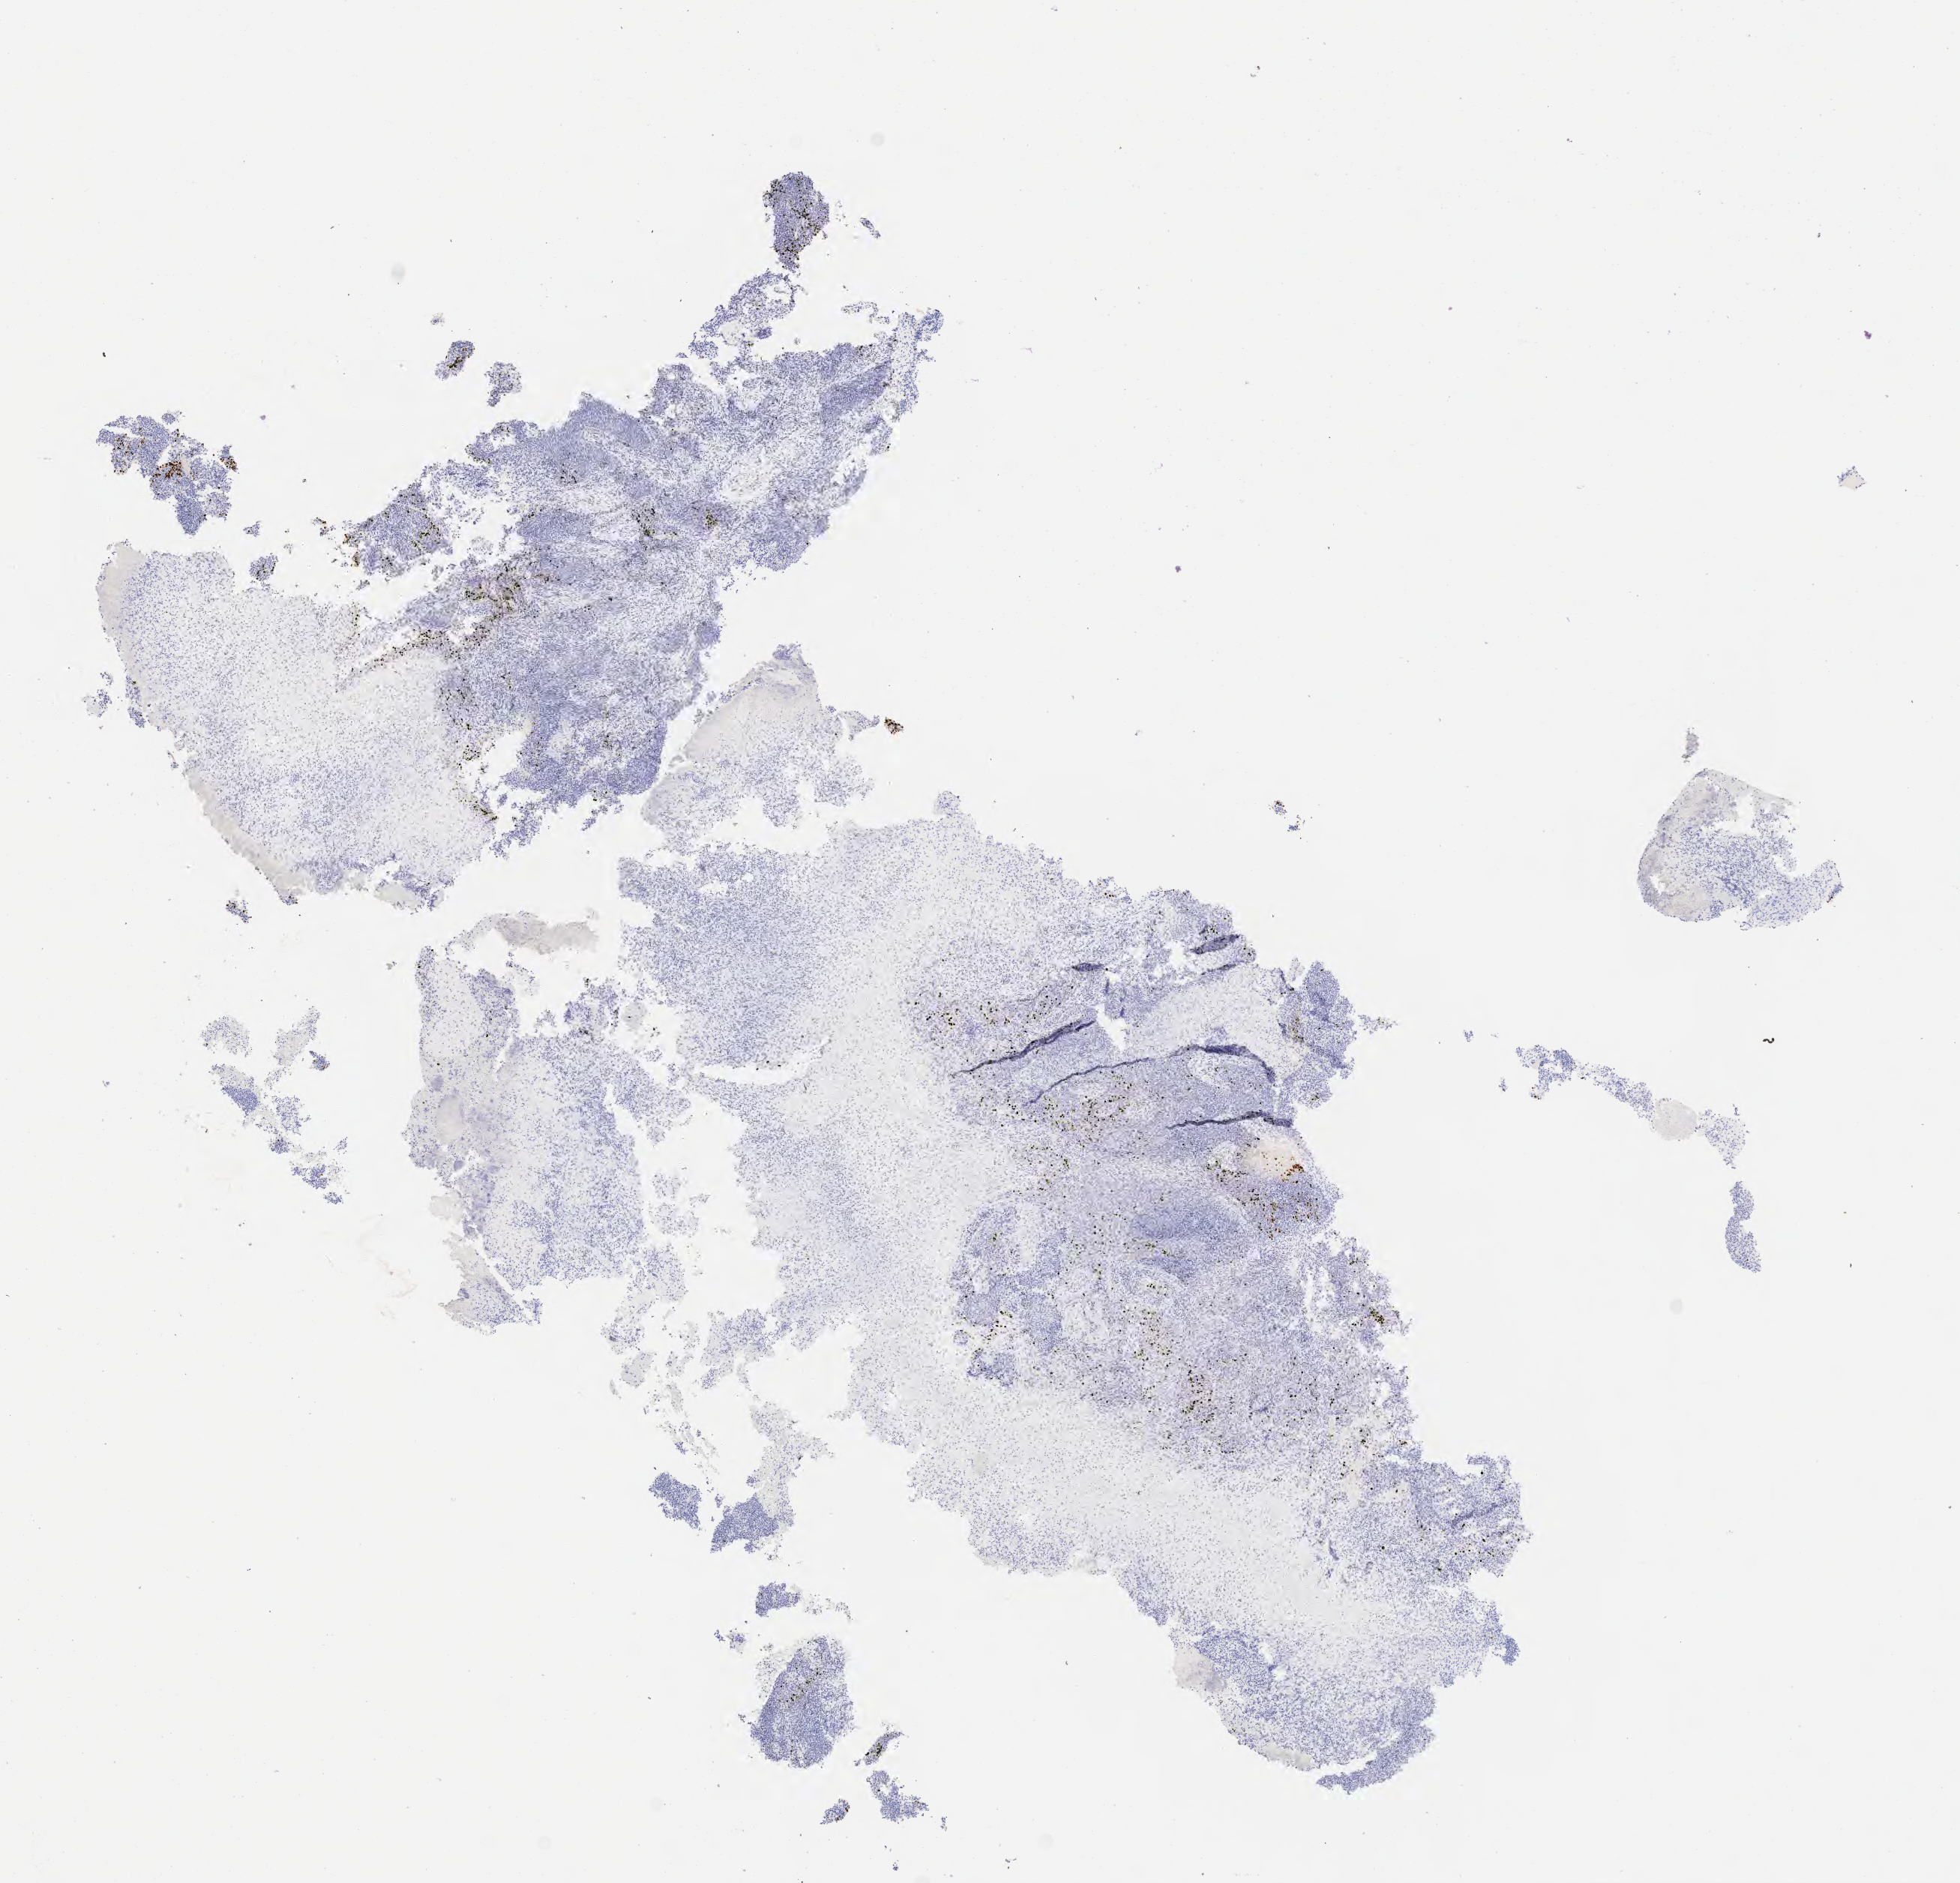
Immunohistochemistry (IHC) whole-slide image stained for p40 — shown as a low-resolution overview of the whole scanned area (about 10.6 x 10.1 mm). Tumor tissue. Anatomic site: cervix. Female patient, aged 65.
Diagnosis: Squamous cell carcinoma, large cell, nonkeratinizing, NOS.